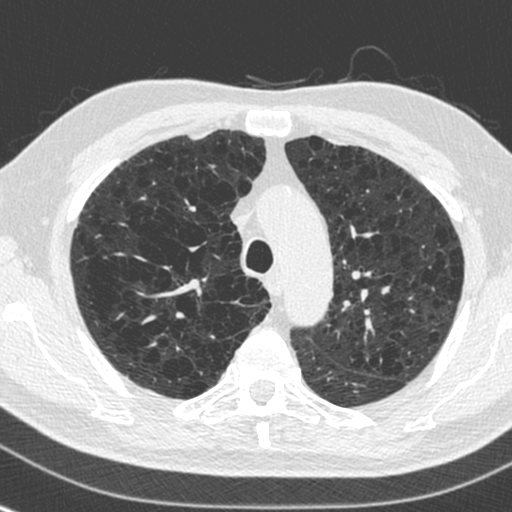
Chest CT (low-dose screening protocol), one axial image; baseline annual screen; lung window (W 1500 / L -600 HU); 1.3 mm slice thickness; standard (soft-tissue) reconstruction kernel (C). Male, age 73 years at enrolment. Current smoker at enrolment.
Expert reader's lesion annotation, bounding box <151,249,198,287> (left, top, right, bottom; pixels). No non-calcified nodule or mass ≥4 mm was recorded by the screening reader at this exam.